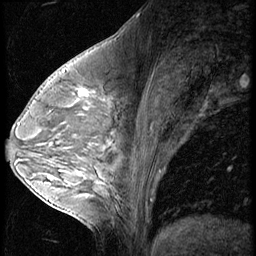
Breast MRI (dynamic contrast-enhanced), one sagittal slice; position 28 of 56 along the scan axis; 3 images stored at this slice position (order not interpretable as contrast timing); 1.5 T; TE 4.2 ms, TR 9 ms; 2.5 mm slice thickness; 256 × 256 image matrix, field of view 180 × 180 mm. Female patient, age 54 years. Case-level facts recorded for this patient, not image findings: setting: breast cancer imaged before/during neoadjuvant chemotherapy; receptor status: triple-negative.
Structures marked on this image (semi-automatically segmented with operator editing):
- analysis volume of interest (the breast-tissue region the enhancement analysis was run in; not a lesion): box from (x=62, y=80) to (x=115, y=128) px
- tumour enhancement mask (voxels above the 140 % enhancement threshold inside the analysis volume of interest): (x=79, y=91)–(x=88, y=97)